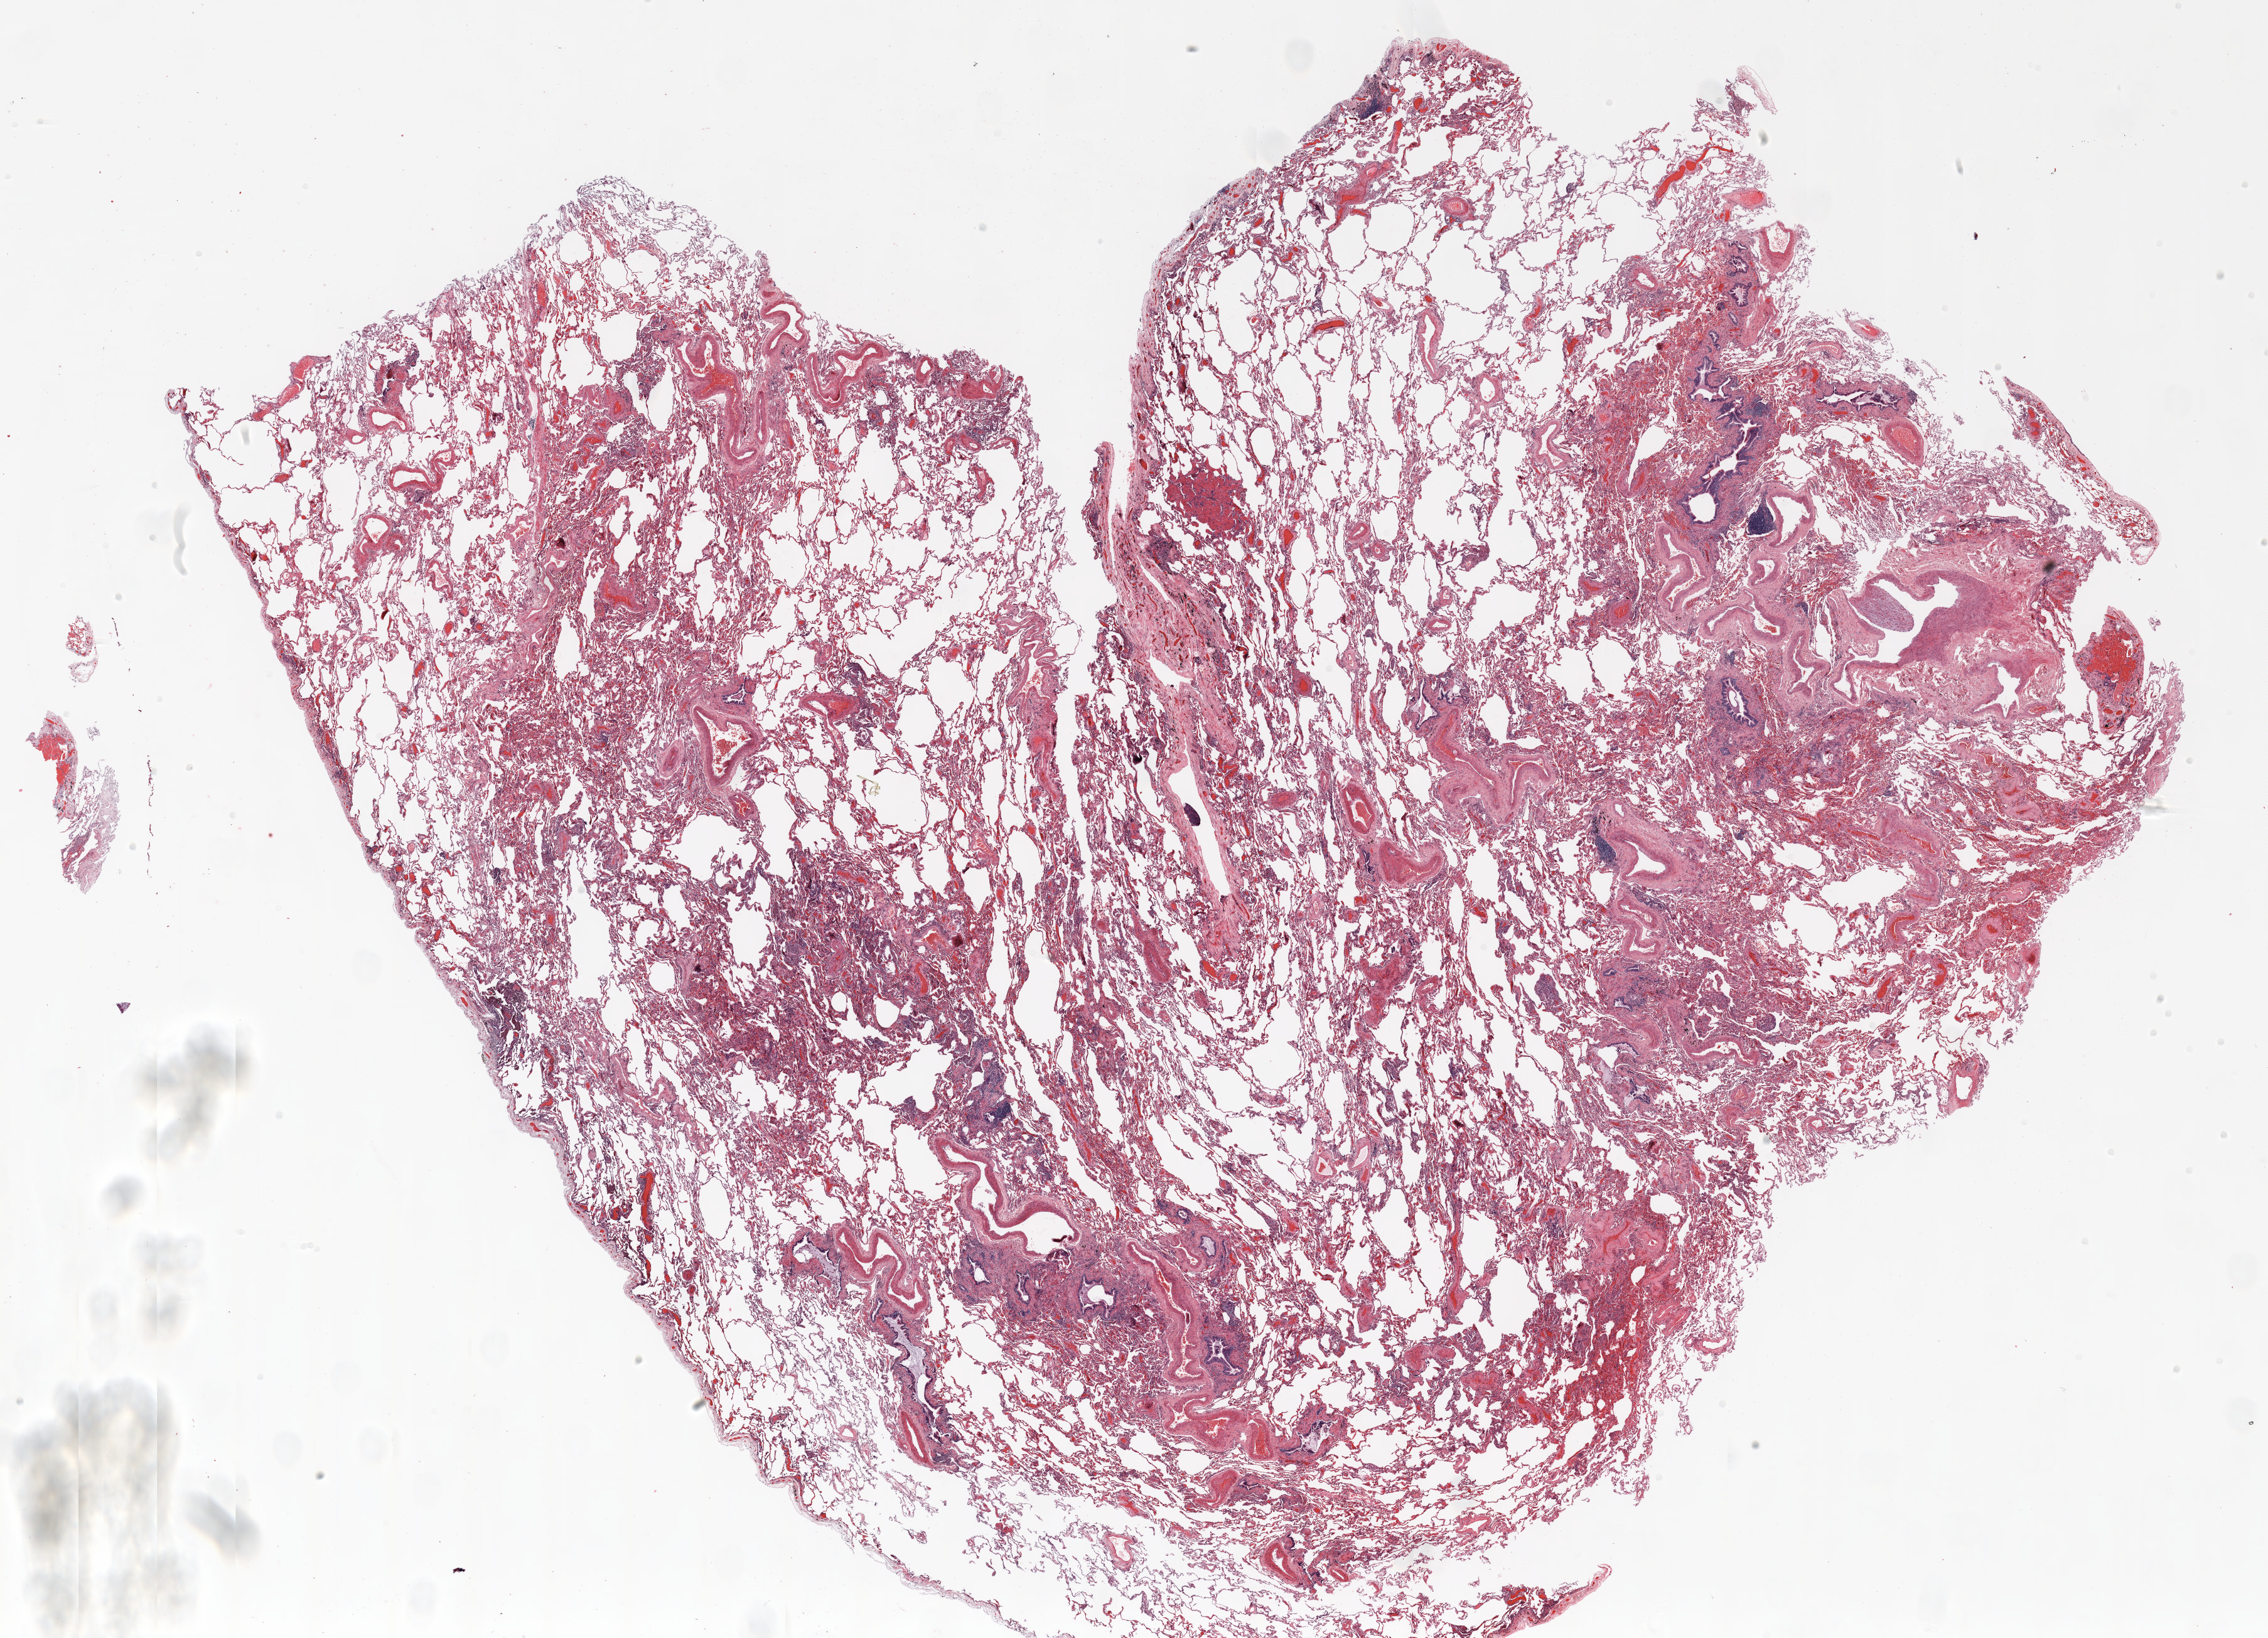
Whole-slide histology image, H&E, shown as a low-resolution overview of the whole scanned area (about 29.0 x 21.0 mm); FFPE section; lung tissue. Male patient, aged 73 at enrolment. Current smoker at enrolment. Grade: poorly differentiated (G3).
* stage (AJCC 6th edition): IA
* tumour size (pathology): 25 mm
* participant's lung-cancer diagnosis: Squamous cell carcinoma, NOS (ICD-O-3 8070/3)
* primary tumour location (clinical record): left lower lobe